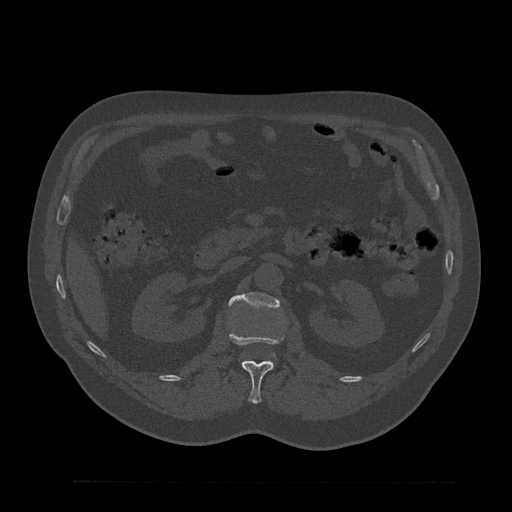
CT including the spine, one axial slice; position 143 of 797 along the scan axis; reconstruction kernel Br40s/3; bone window (W 1800 / L 400 HU); 0.5 mm slice thickness; 512 × 512 image matrix. Patient: male, 61 years. From the clinical record (not read from this slice): primary cancer: prostate.
Annotated regions visible in this slice (semi-automatically segmented with operator editing):
- L1 vertebra: box from (x=229, y=332) to (x=284, y=404) px
- L2 vertebra: (x=228, y=292)–(x=280, y=307)